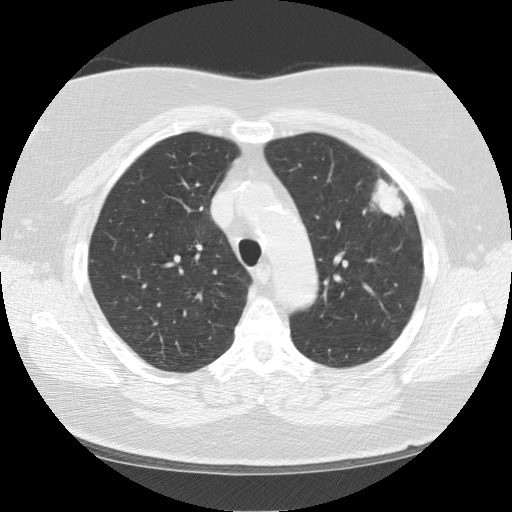
Low-dose screening chest CT, one axial slice. 120 kVp. Lung window (W 1500 / L -600 HU). 512 × 512 image matrix, field of view 350 × 350 mm.
Structures marked on this image (expert manual segmentation):
- lesion 1 (tumor, upper lobe of left lung): box from (x=372, y=179) to (x=404, y=217) px